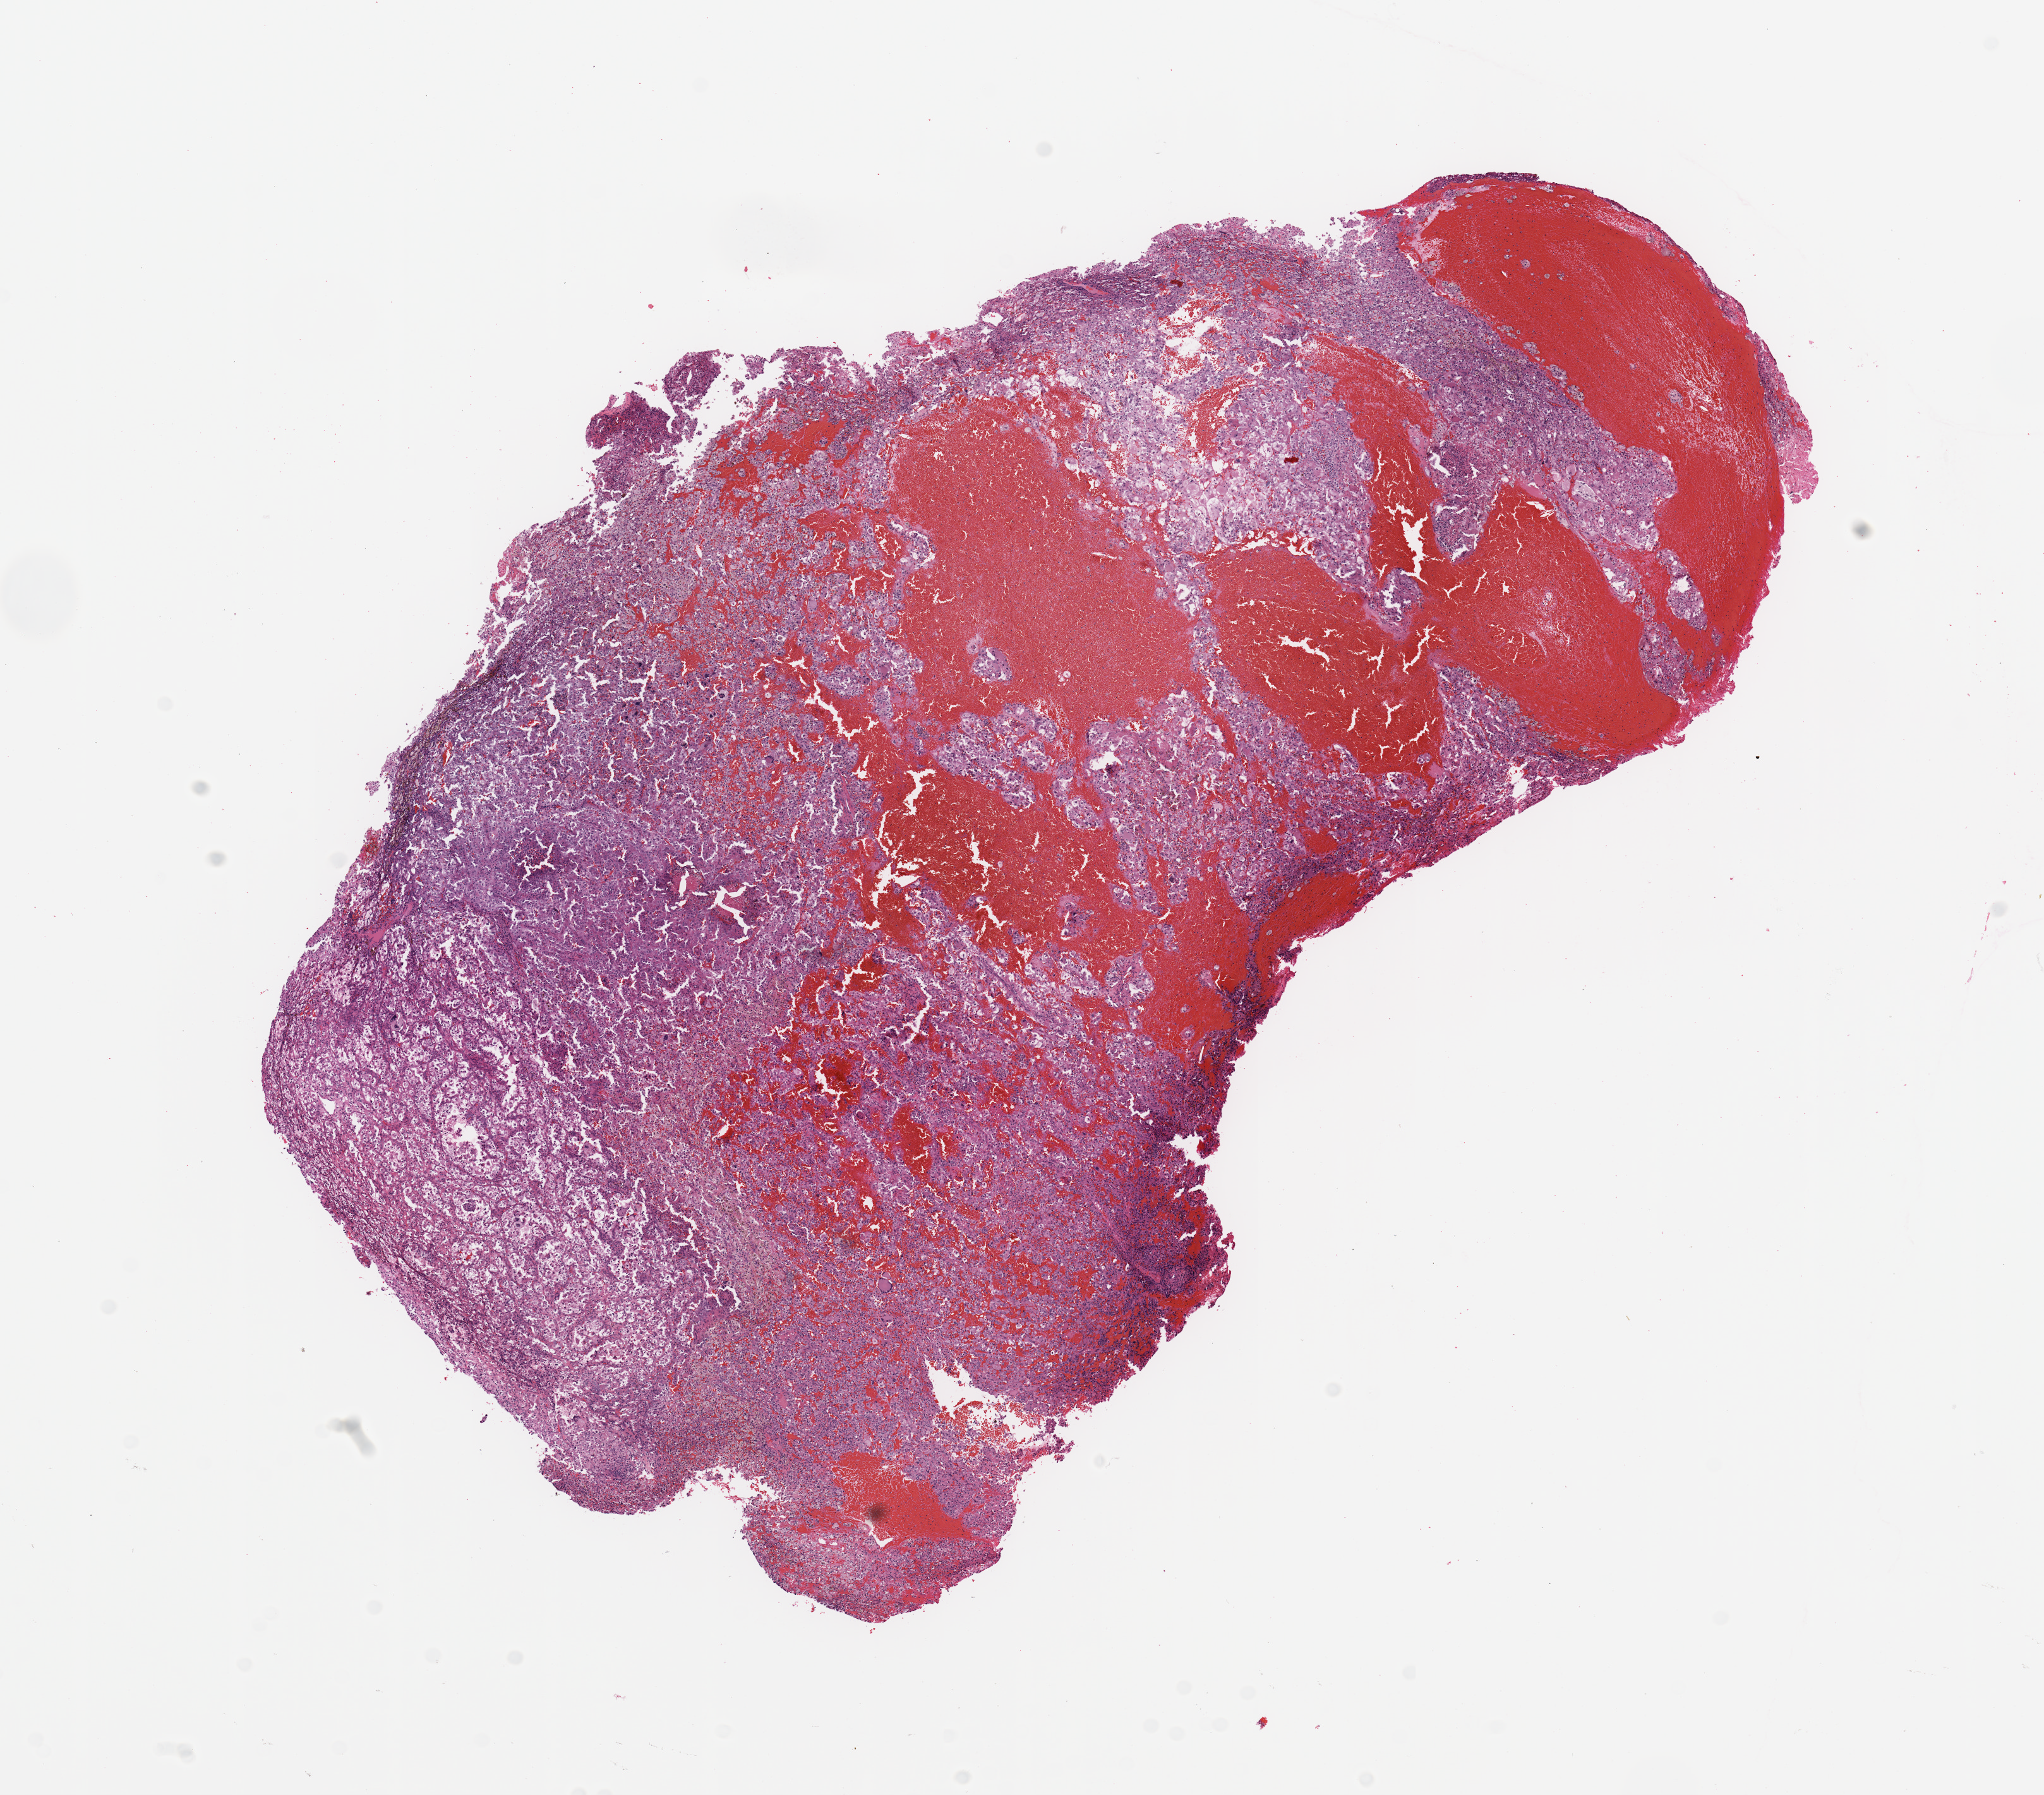
Hematoxylin and eosin (H&E) stained whole-slide image, shown as a low-resolution overview of the whole scanned area (about 12.8 x 11.2 mm, slide scanned at 20x); kidney, tumour tissue. 68-year-old male patient. Histologic grade: G4 (undifferentiated).
- AJCC pathologic stage: IV
- diagnosis: Renal cell carcinoma, NOS